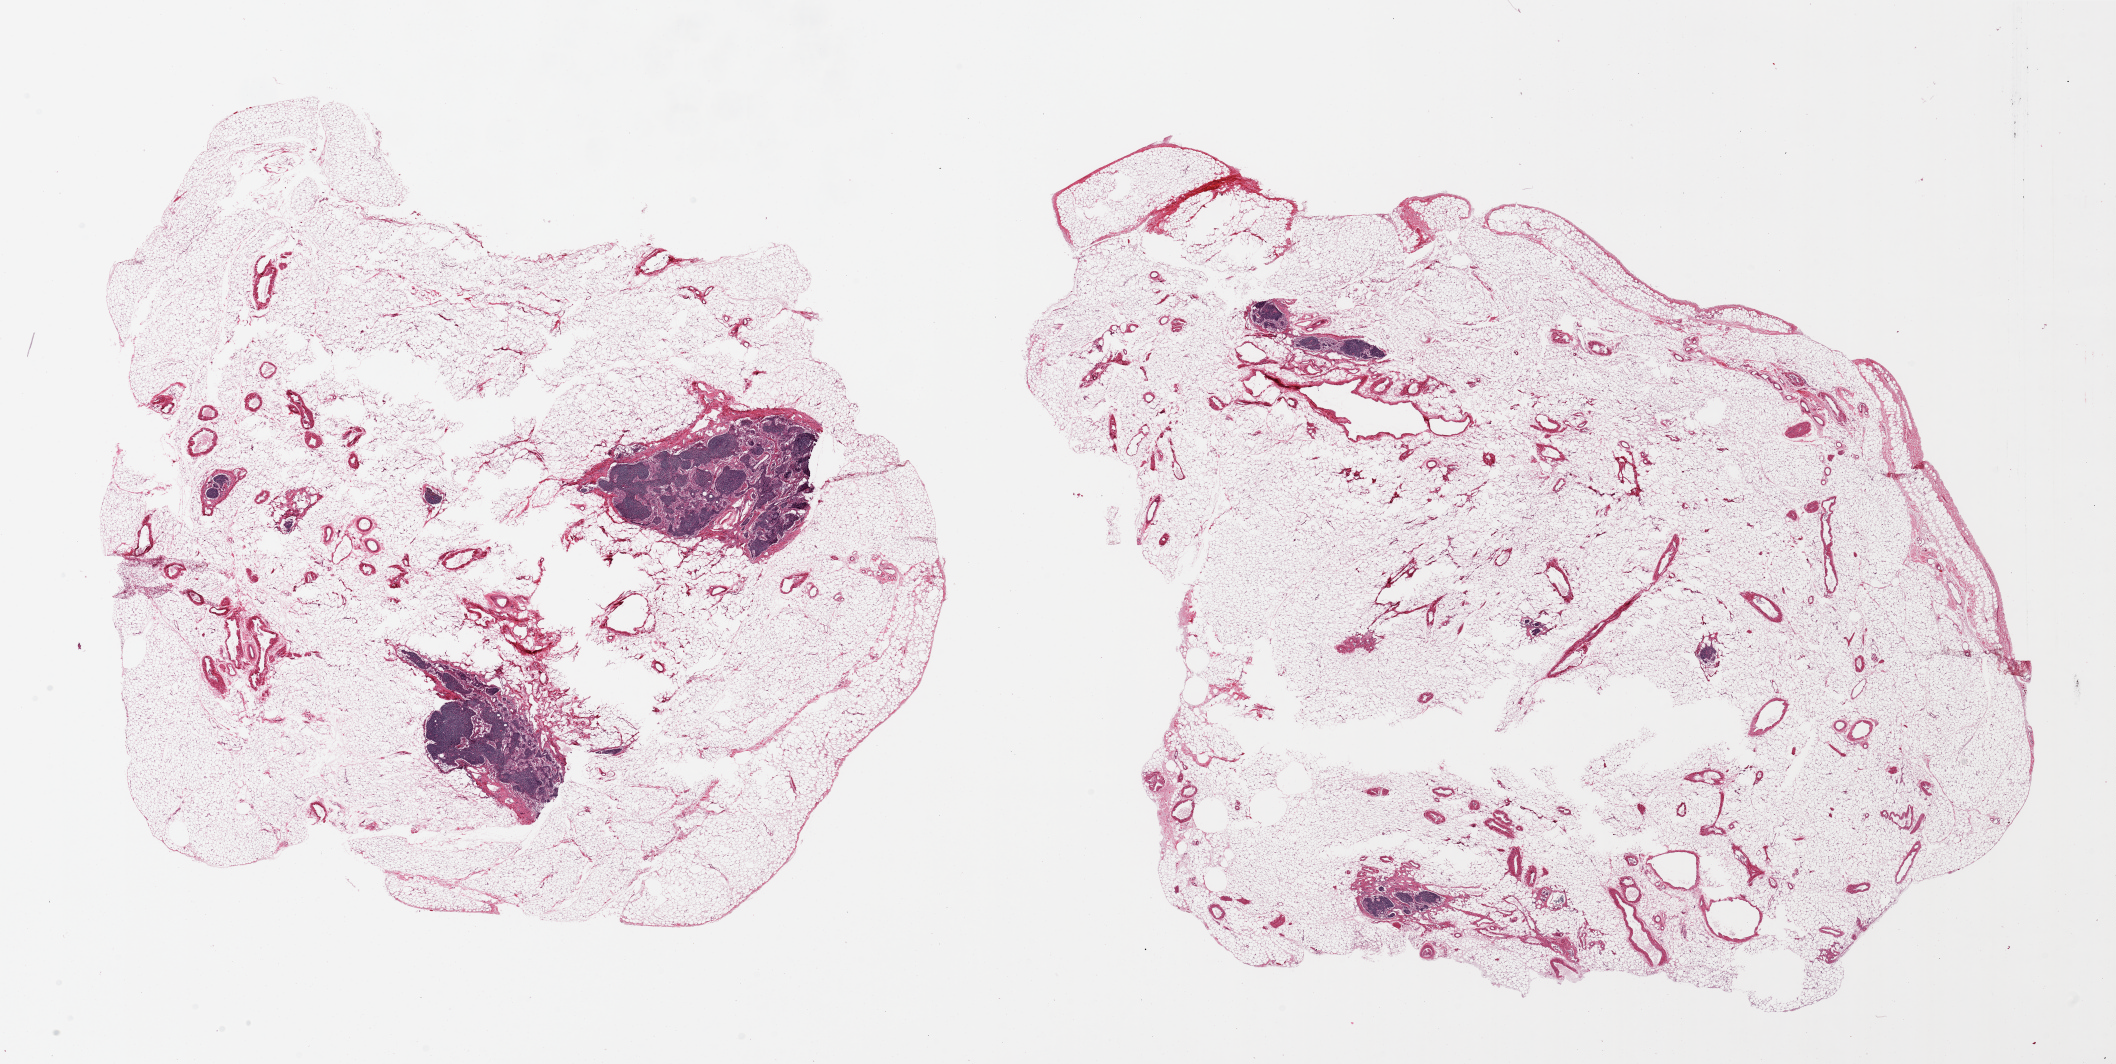
H&E whole-slide image, brightfield, low-resolution overview of the scanned area, about 33.5 x 16.8 mm (slide scanned at 20x). PAXgene-fixed, paraffin-embedded tissue. Target tissue: omentum. Tissue donor sample. Donor: male.
* pathologist's review note for this sample: 2 pieces; large pieces contain central holes; also have lymph nodes and lymph nodules